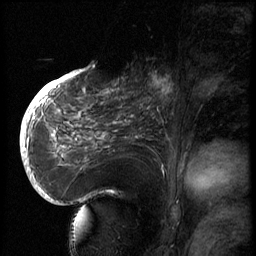
Breast MRI (dynamic contrast-enhanced), one sagittal slice; position 32 of 66 along the scan axis; 3 images stored at this slice position (order not interpretable as contrast timing); 1.5 T; TE 4.2 ms, TR 8.9 ms; 256 × 256 image matrix, field of view 200 × 200 mm. Patient: female, 56 years. Case-level facts recorded for this patient, not image findings: setting: breast cancer imaged before/during neoadjuvant chemotherapy.
Structures marked on this image (semi-automatically segmented with operator editing):
- analysis volume of interest (the breast-tissue region the enhancement analysis was run in; not a lesion): bounding box [x1, y1, x2, y2] px = [129, 62, 194, 127]
- tumour enhancement mask (voxels above the 140 % enhancement threshold inside the analysis volume of interest): [149, 71, 175, 111]